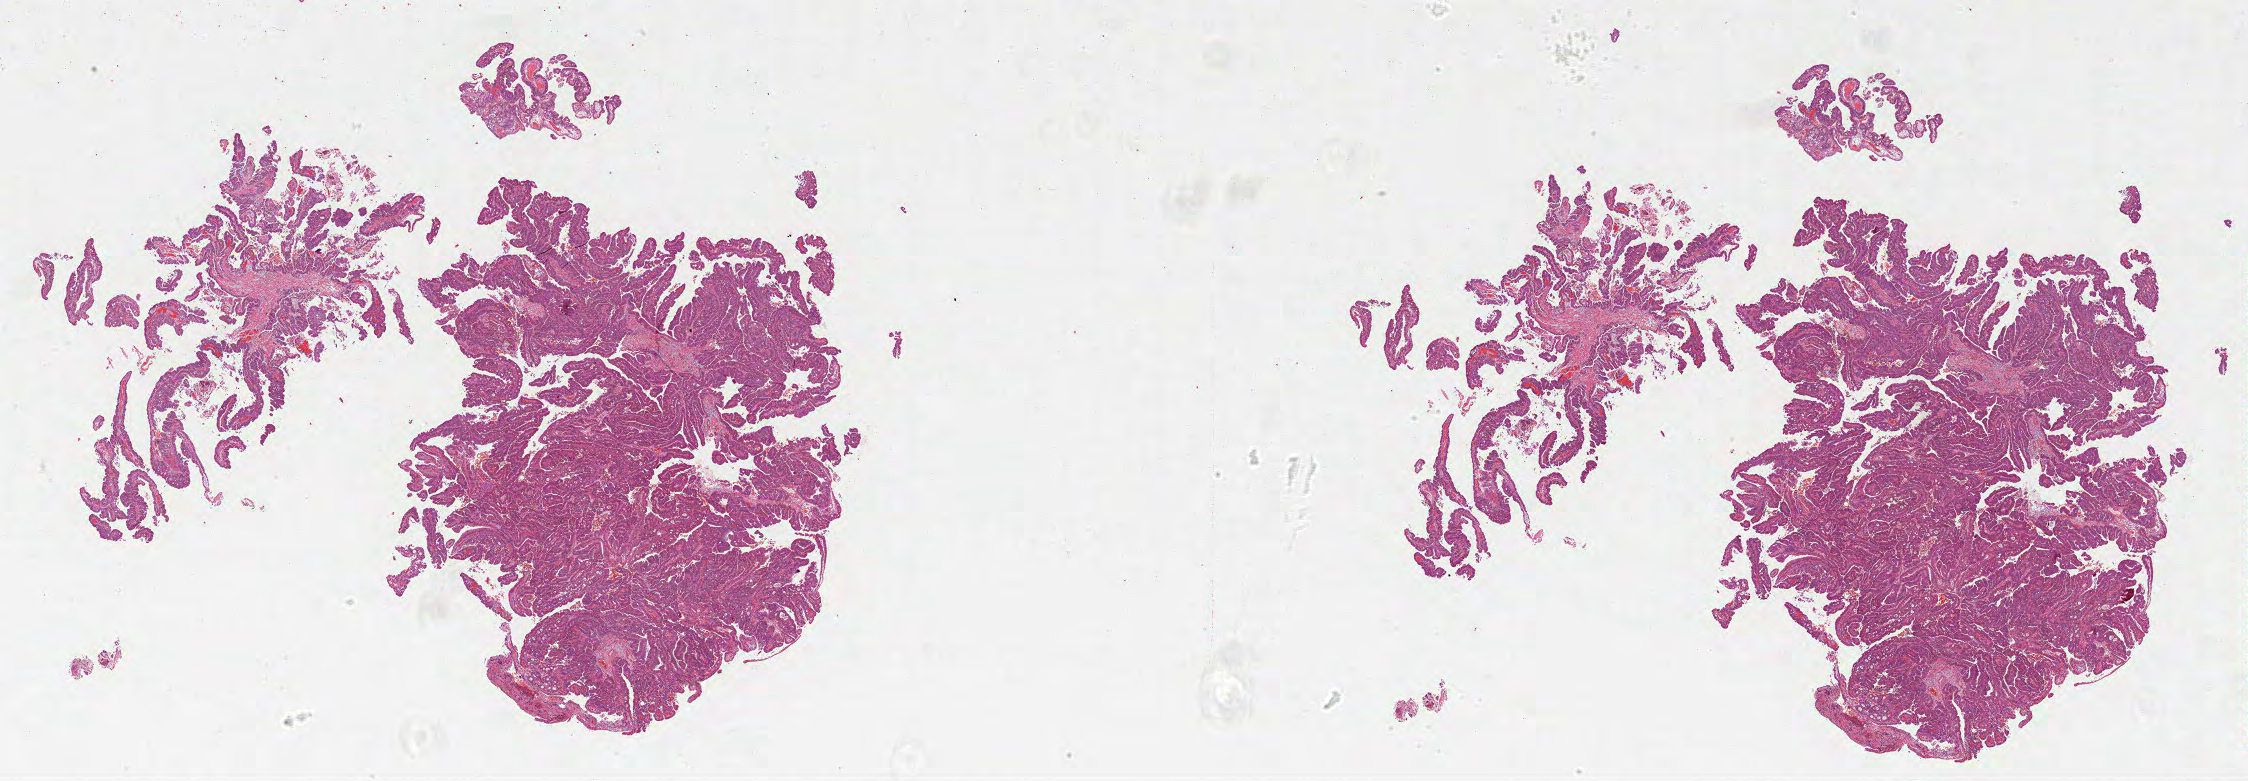
Hematoxylin and eosin (H&E) stained whole-slide image — low-resolution overview of the scanned area, about 36.0 x 12.5 mm, formalin-fixed paraffin-embedded (FFPE) diagnostic section, sample: primary tumour, bladder. Female, age 52 years at initial diagnosis. Histologic grade: high grade.
Lymph nodes positive (case pathology): 0 of 10 examined. AJCC pathologic stage: III (6th edition). Diagnosis: Papillary adenocarcinoma, NOS (dome of bladder).